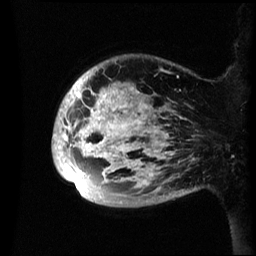
Breast MRI (dynamic contrast-enhanced), one sagittal slice; slice 9 of 60 in the series (ordered by position); dynamic contrast-enhanced series, image 2 of 3 at this slice position (ordered by acquisition); 1.5 T; TE 4.2 ms, TR 8.4 ms; 256 × 256 image matrix. Patient: female, 48 years.
Outlined on this slice (semi-automatically segmented with operator editing):
- analysis volume of interest (the breast-tissue region the enhancement analysis was run in; not a lesion): bounding box (x1, y1, x2, y2) in pixels: (52, 56, 195, 207)
- tumour enhancement mask (voxels above the 70 % enhancement threshold inside the analysis volume of interest): (52, 81, 174, 194)